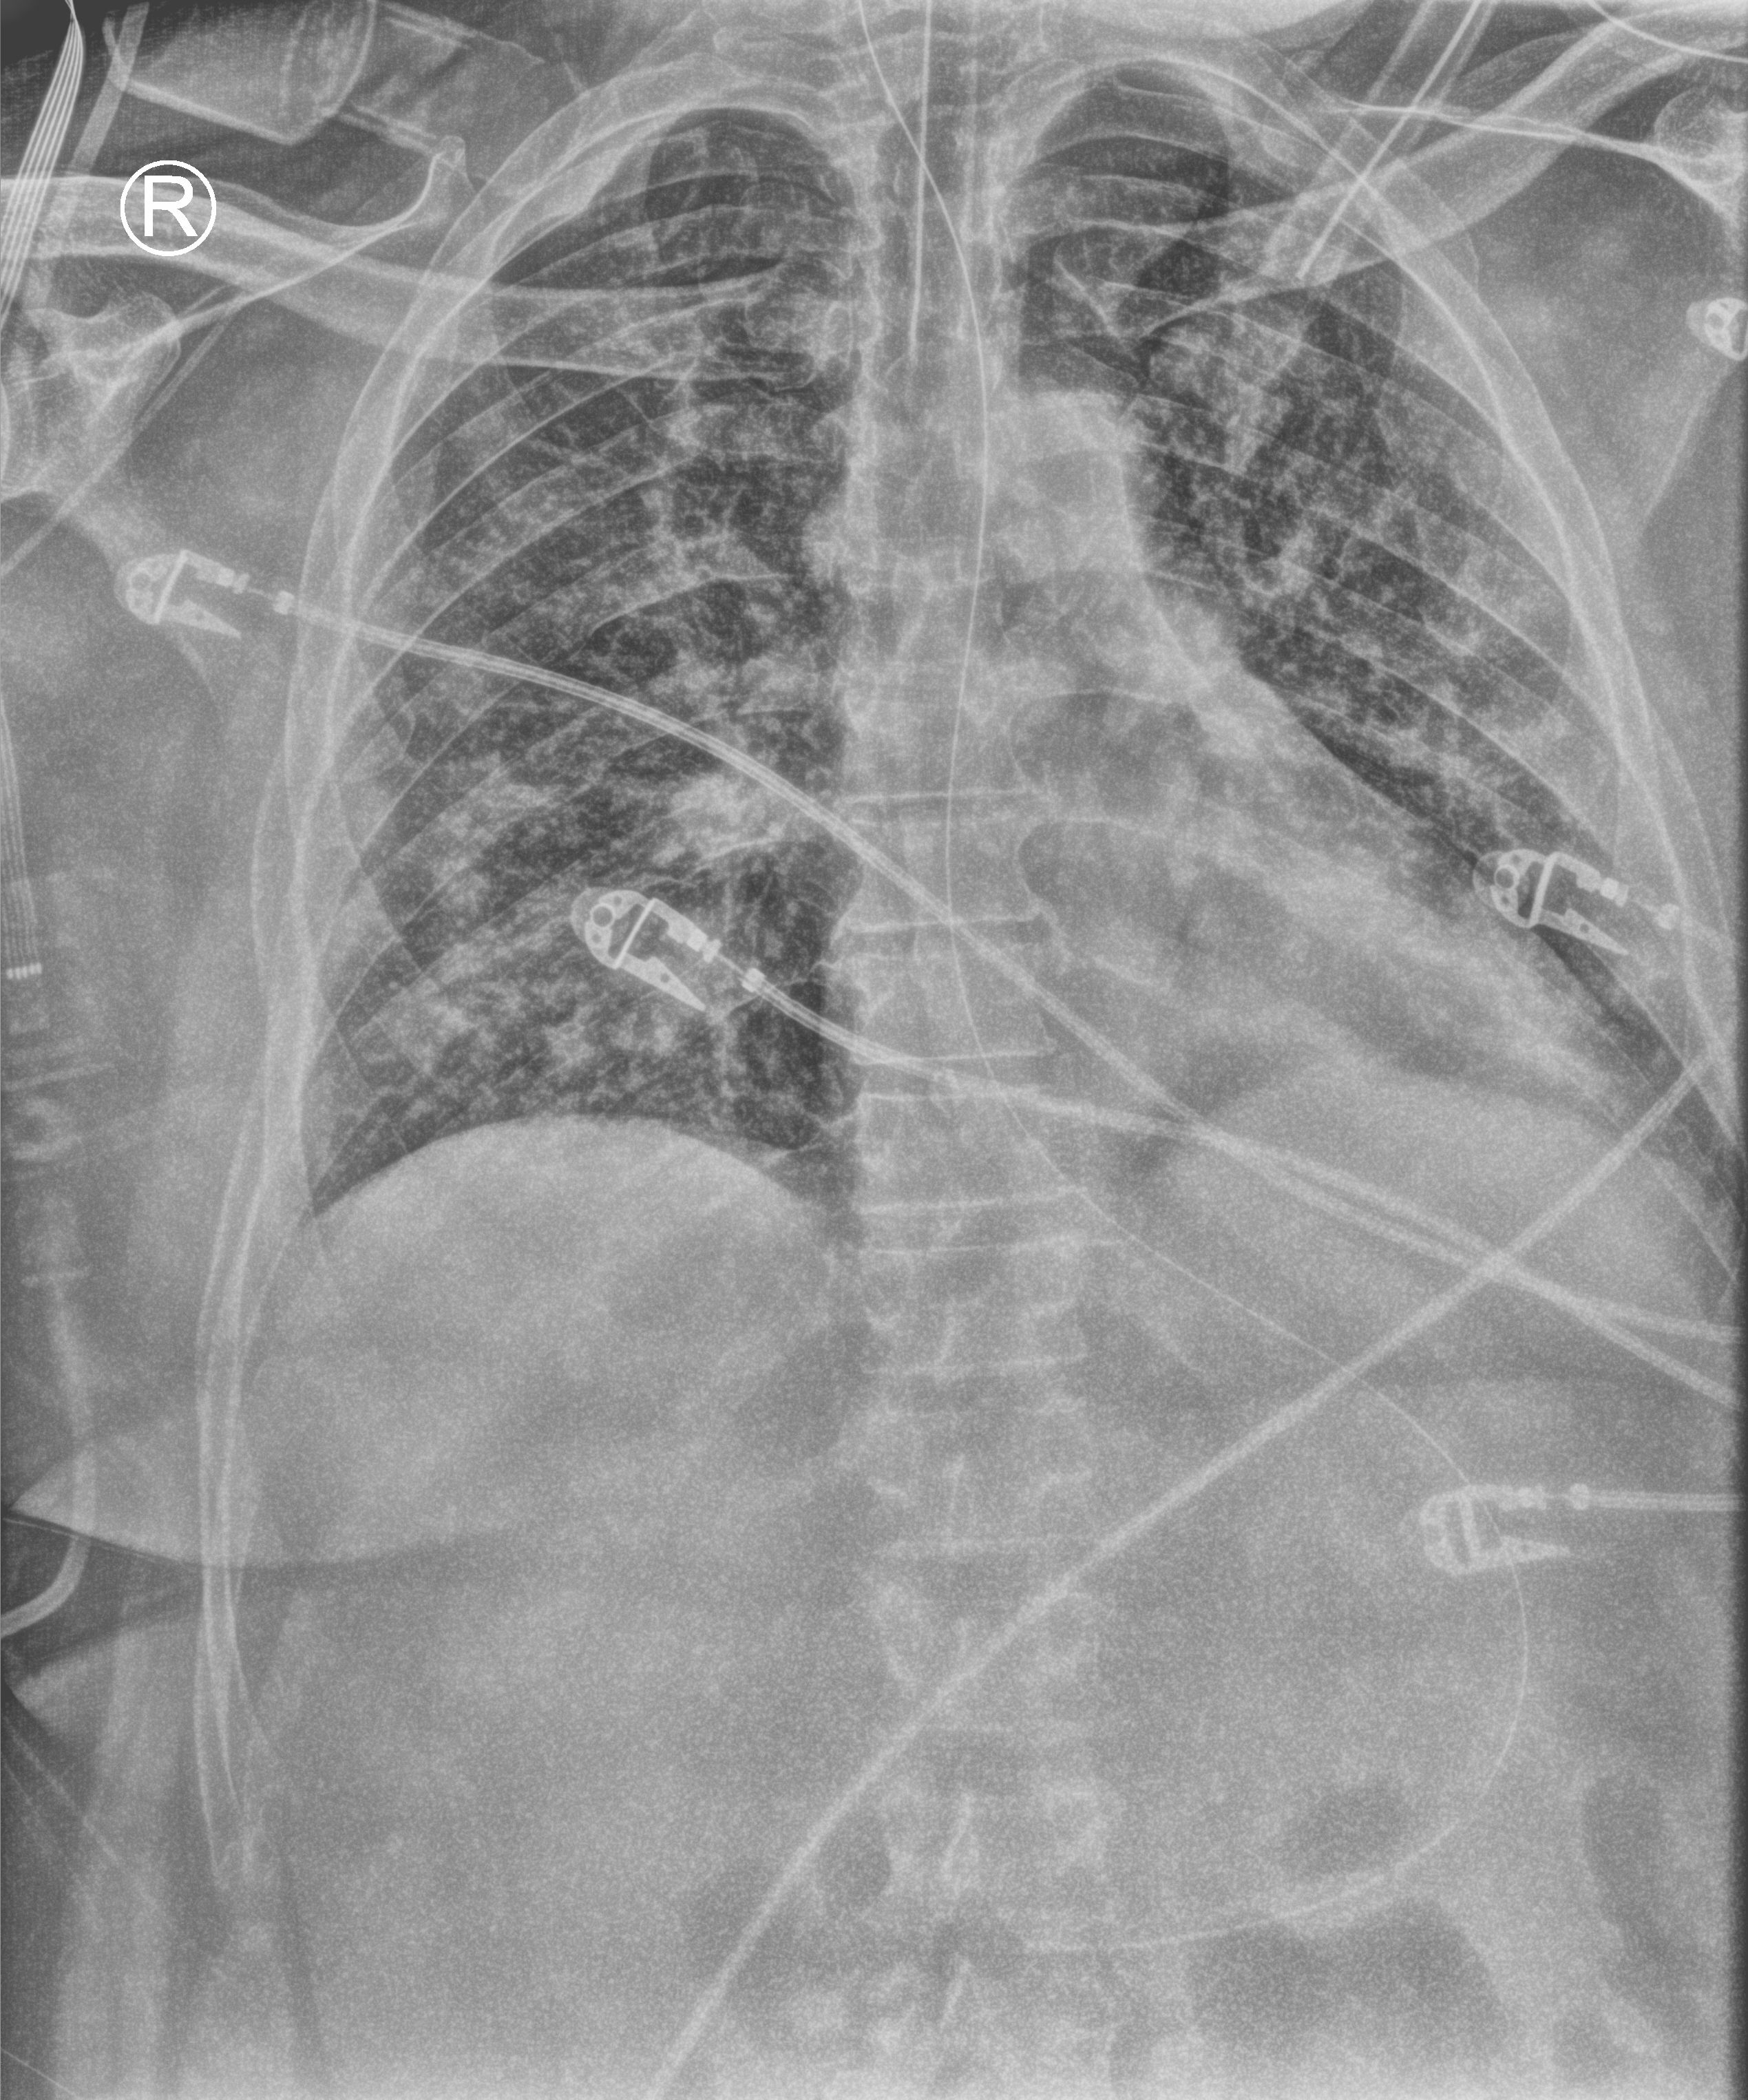
Portable chest radiograph, anteroposterior (AP) projection. Patient hospitalised with COVID-19; male, aged 18–59 years.
From the hospital-stay record, not from the radiograph (when in the stay this image was taken is not recorded):
- mechanically ventilated during this hospital stay: yes